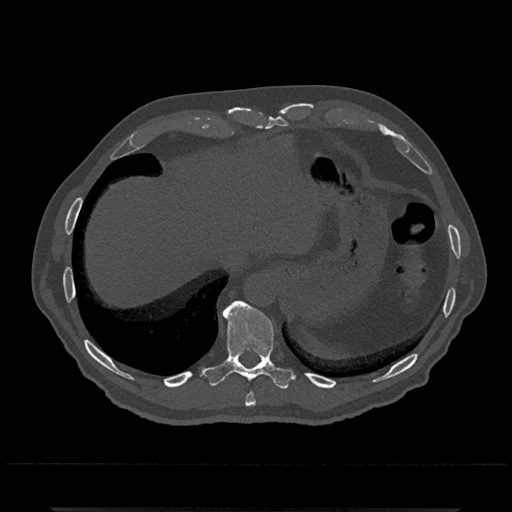
CT including the spine, one axial slice; bone window (W 1800 / L 400 HU); 0.5 mm slice thickness; 512 × 512 image matrix, field of view 393 × 393 mm. Male patient, age 67 years. From the clinical record (not read from this slice): primary cancer: prostate.
Structures marked on this image (semi-automatic segmentation, software-assisted and operator-edited):
- T10 vertebra: bounding box <203,300,294,389> (left, top, right, bottom; pixels)
- T9 vertebra: <245,392,256,407>